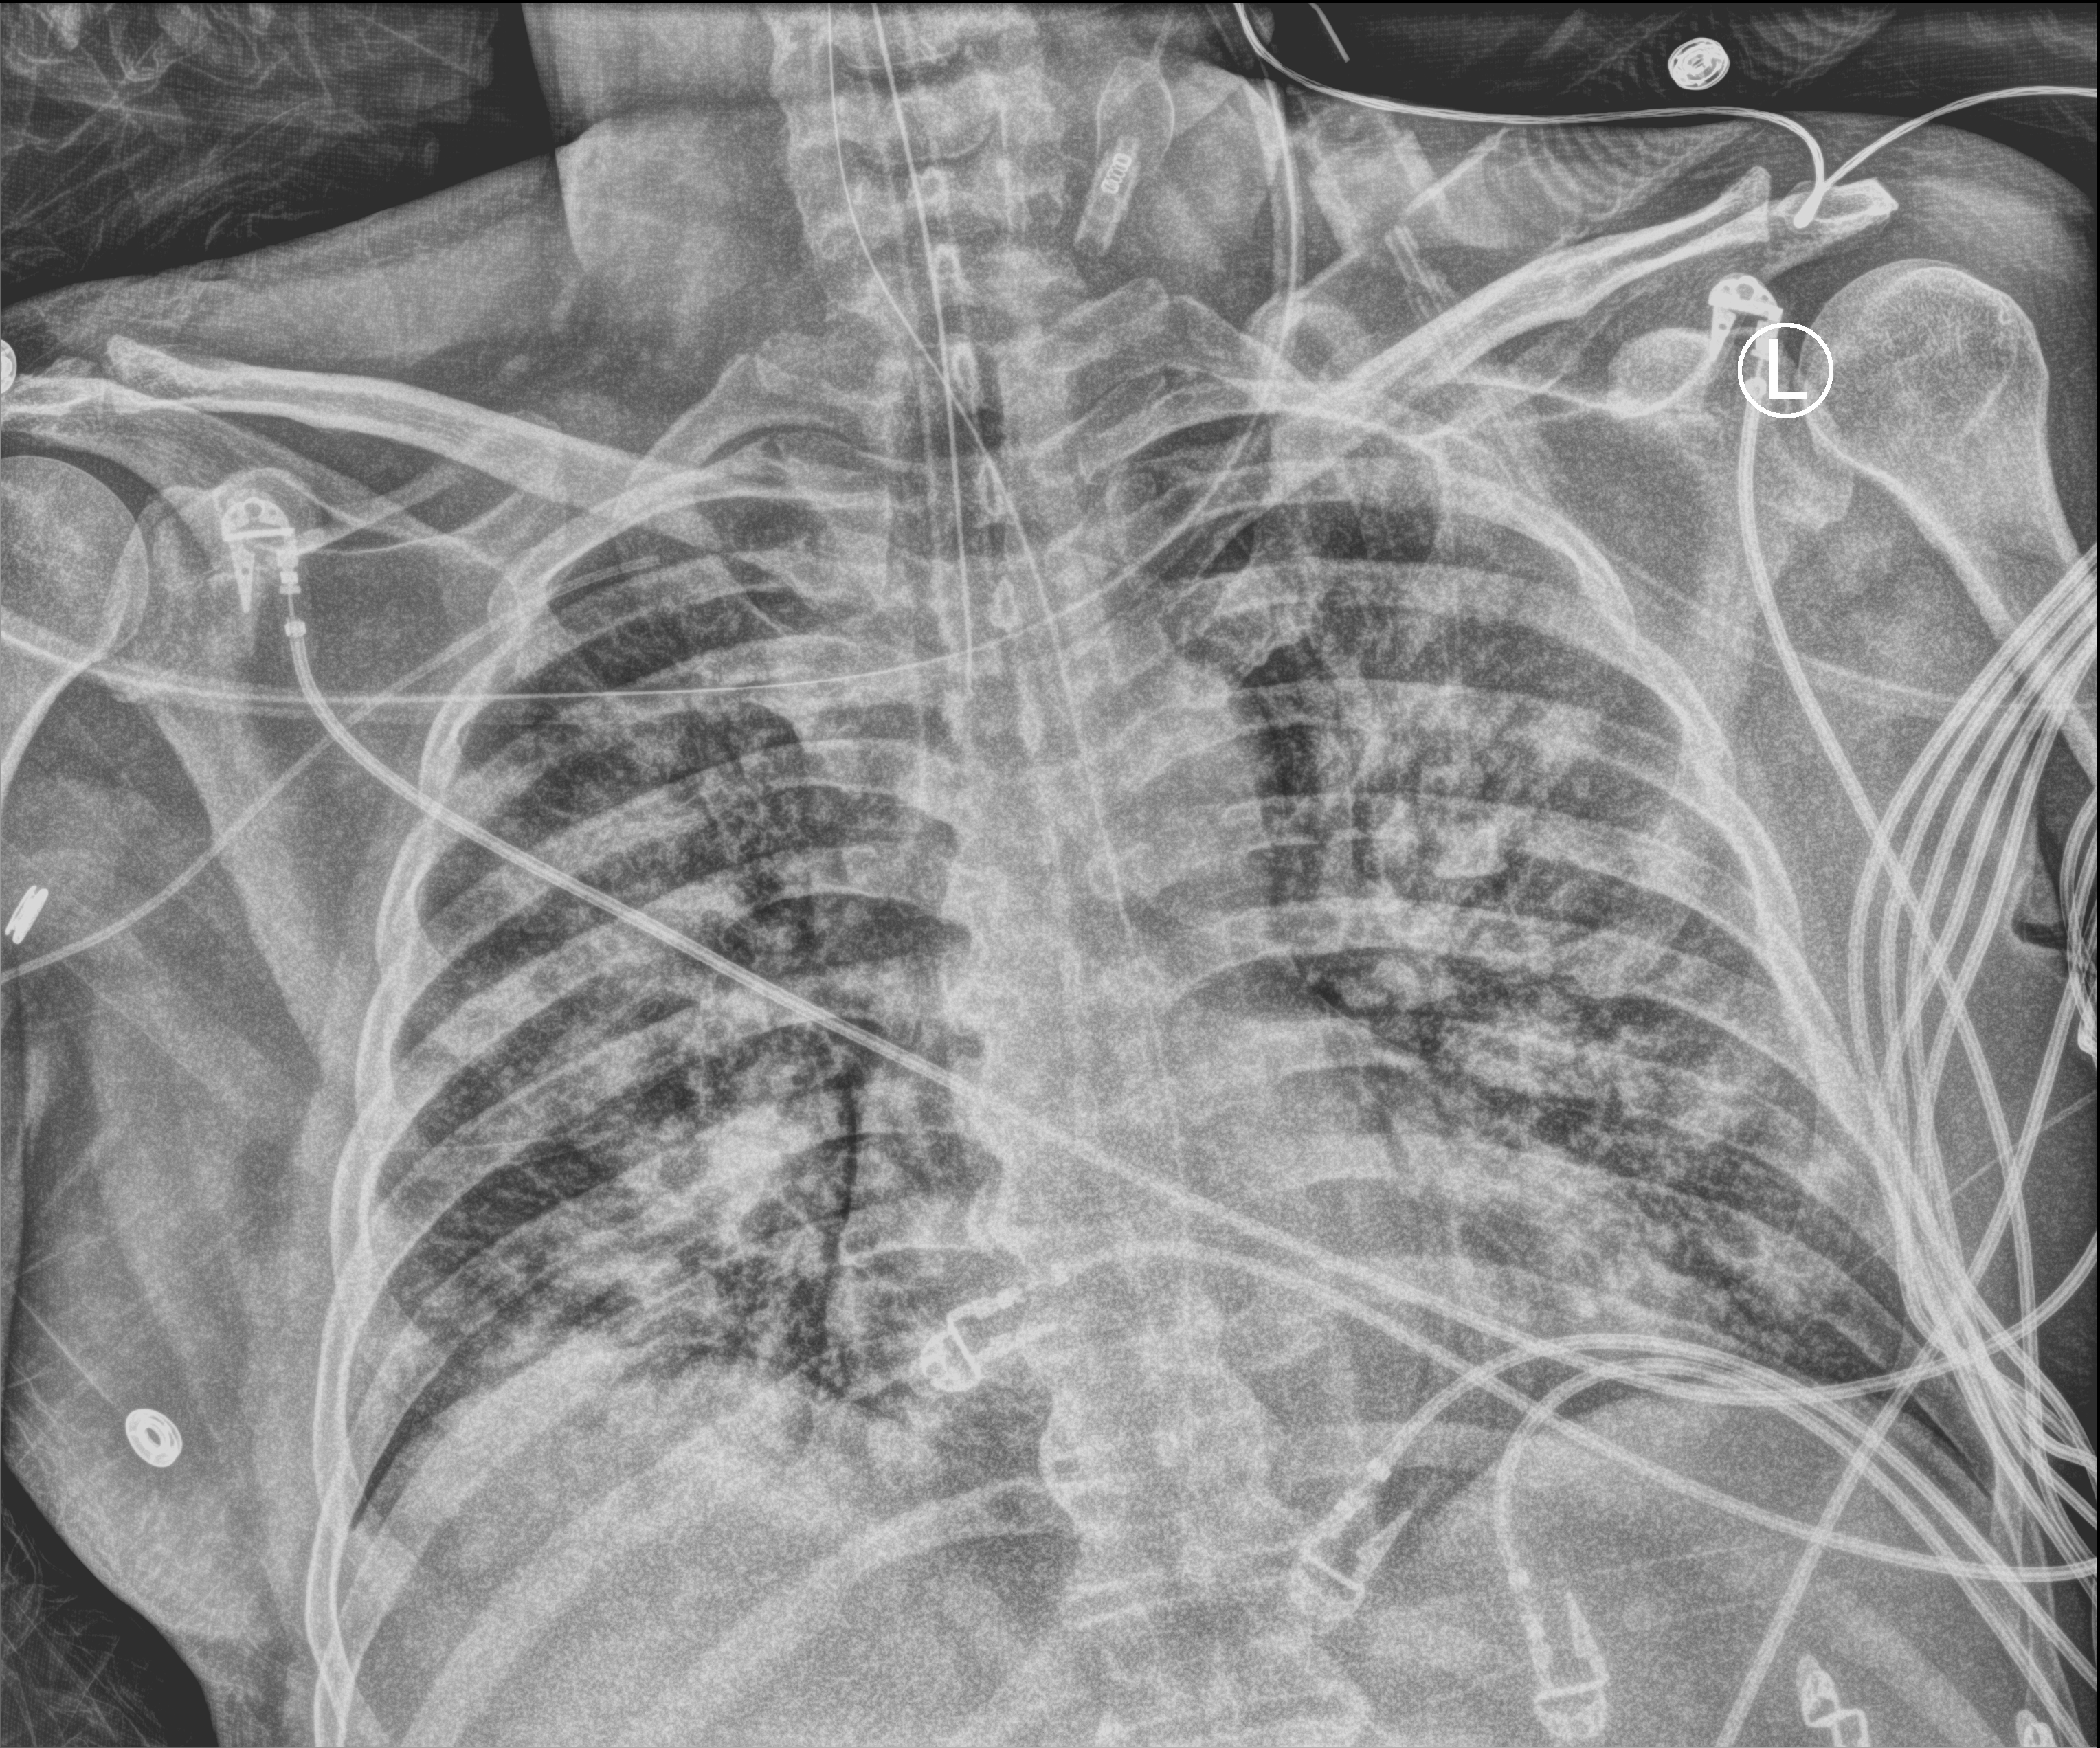
Portable chest radiograph; anteroposterior (AP) projection. Male patient hospitalised with COVID-19, age 18–59 years.
Admission-level facts for this patient (not findings on this image; timing relative to this image not recorded):
- smoking status (admission record): never
- admitted to intensive care during this hospital stay: yes
- hypertension (admission record): yes